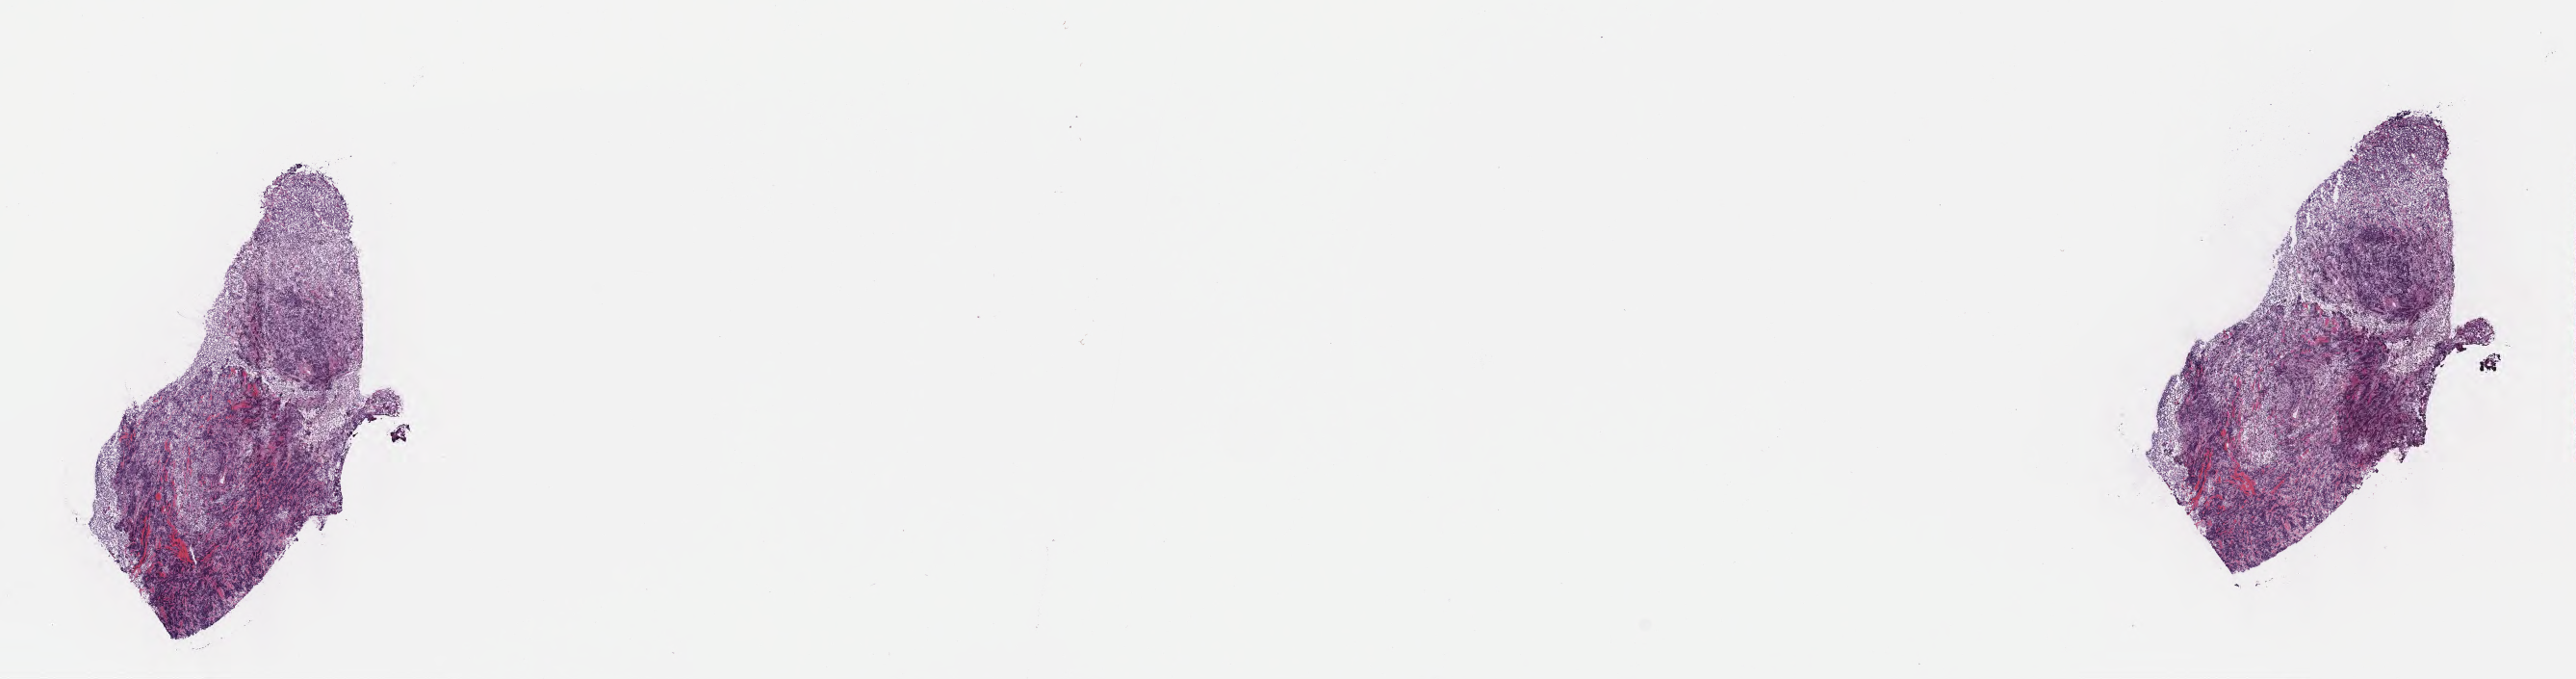
Haematoxylin and eosin whole-slide image, whole scanned area (about 21.6 x 5.7 mm) shown as a low-resolution overview. Frozen section. Primary tumor. Site: head and neck. Male, age 4 years at initial diagnosis. Pathologist review of this section (percent, as recorded): tumor cells 75%, tumor nuclei 85%.
Diagnosis: Burkitt lymphoma, NOS.